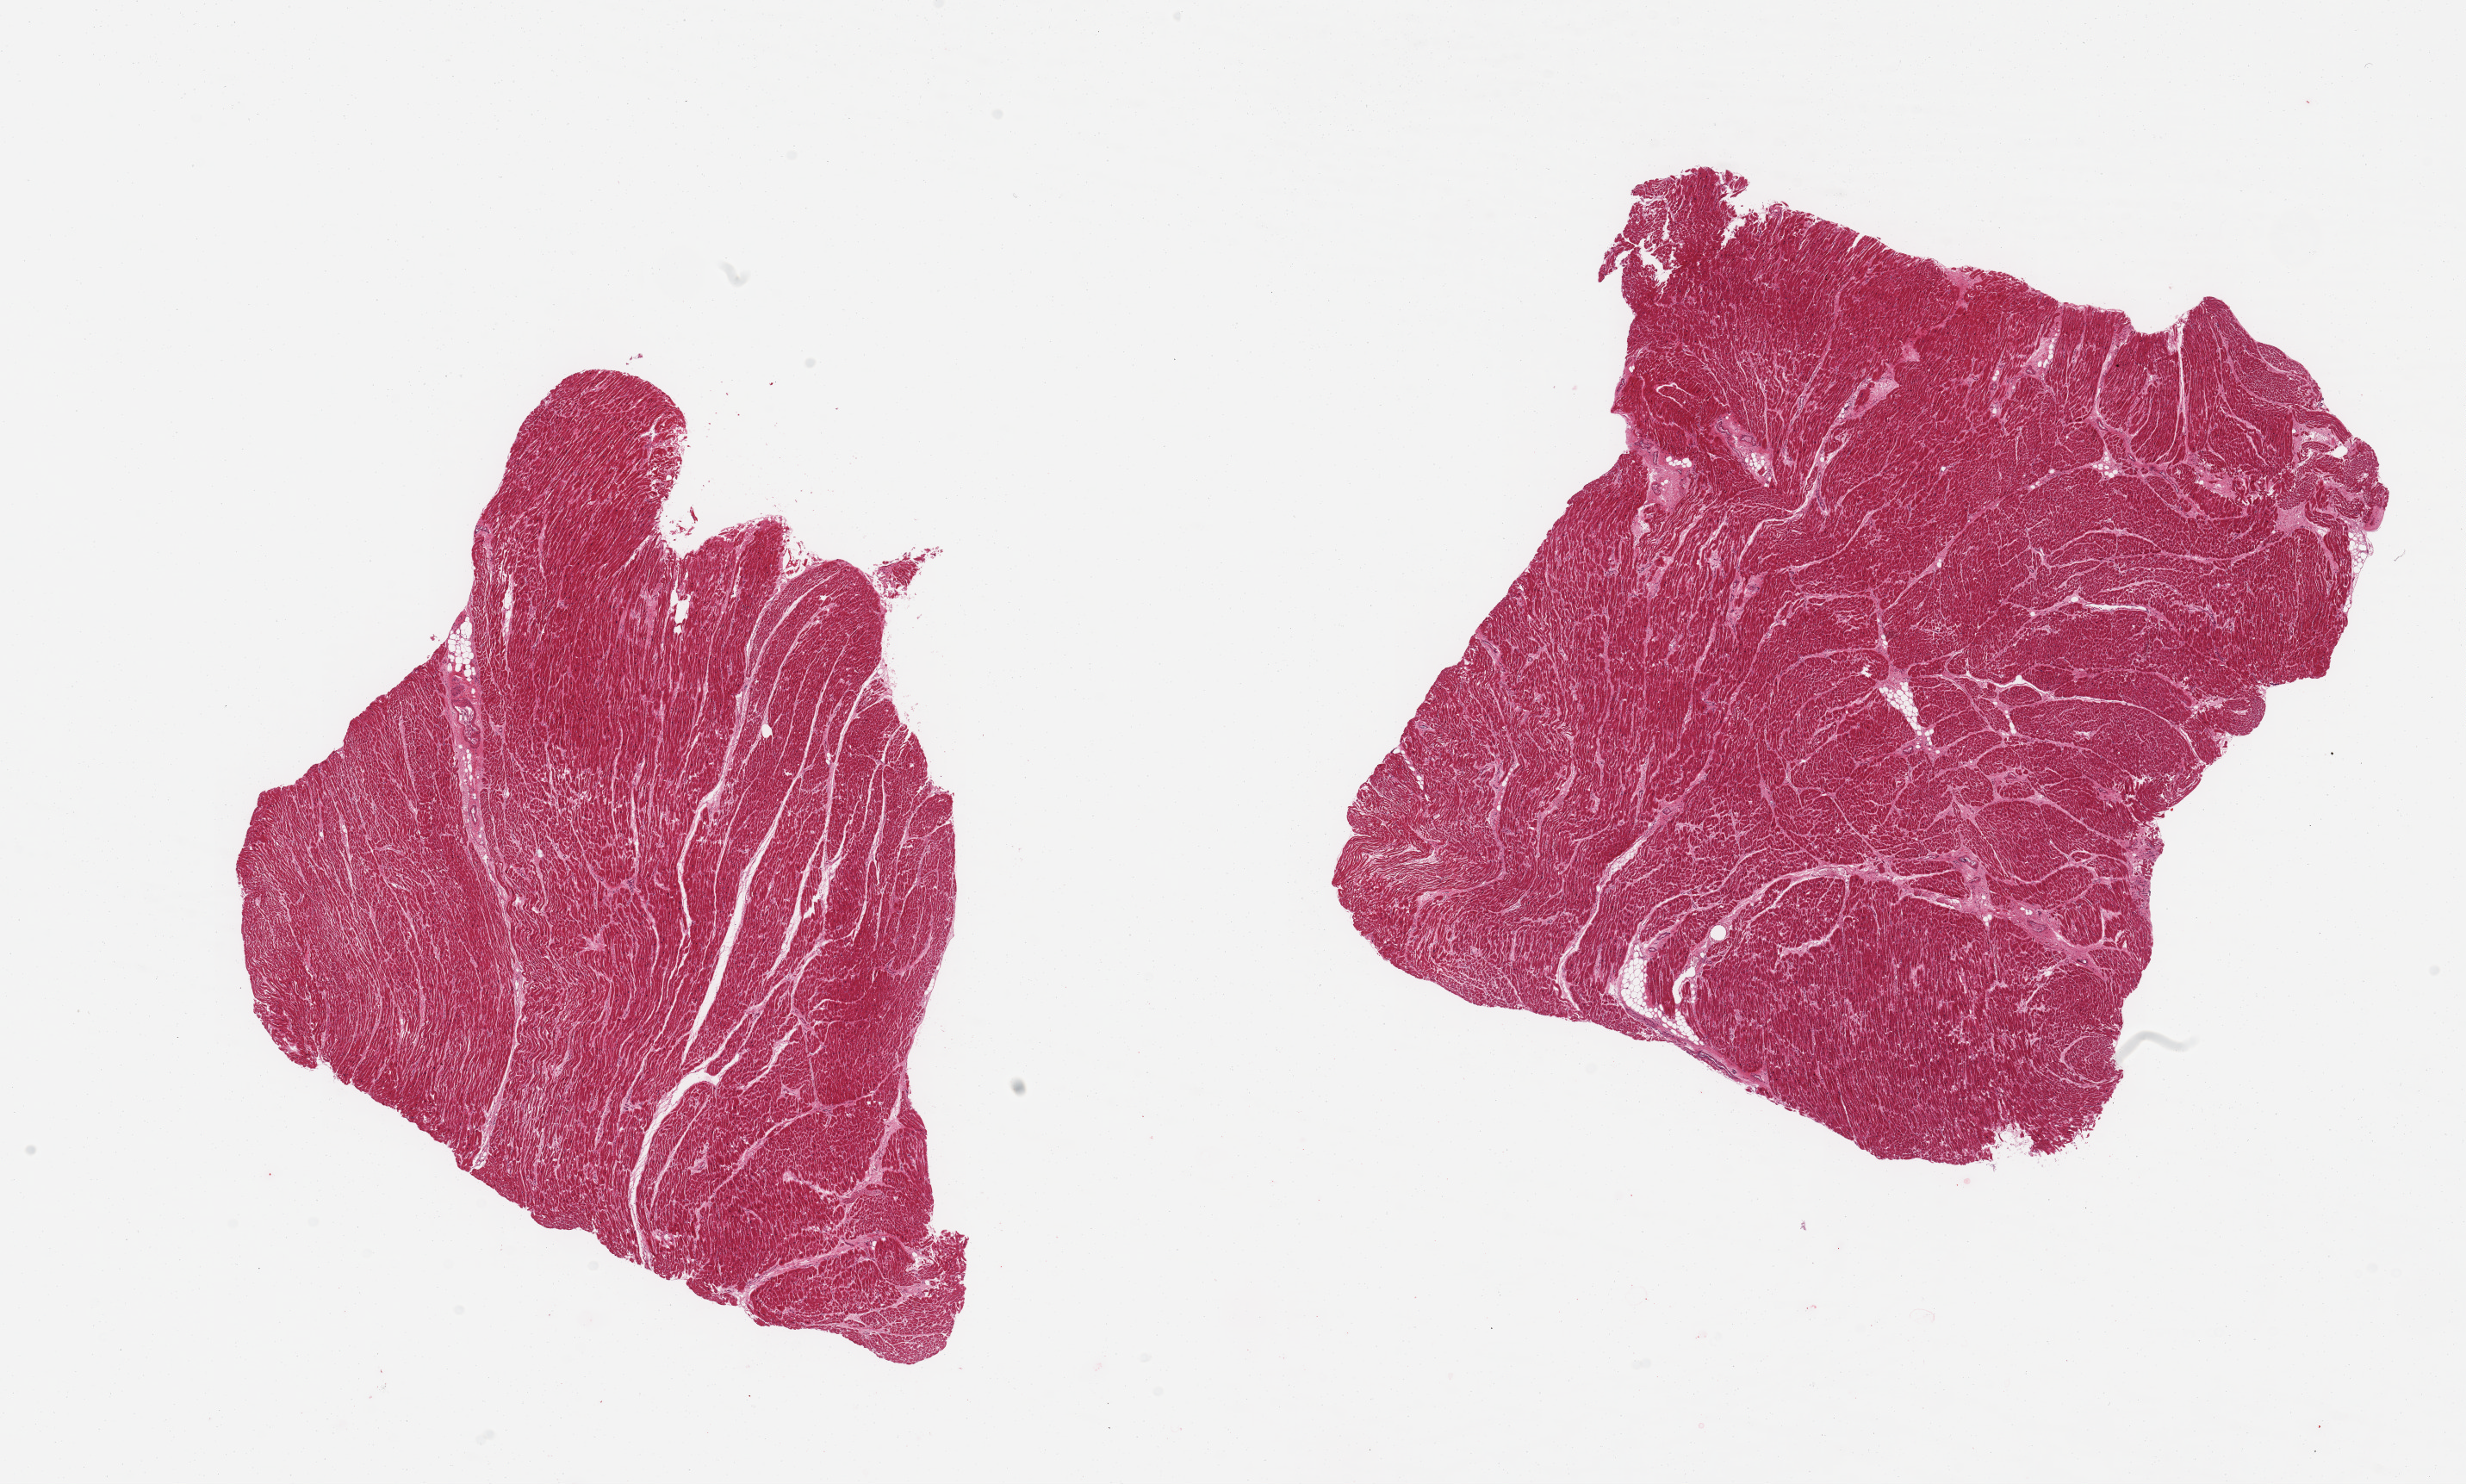
Whole-slide image, hematoxylin and eosin (H&E) stain, brightfield — shown as a low-resolution overview of the whole scanned area (about 22.6 x 13.6 mm); PAXgene-fixed, paraffin-embedded tissue; target tissue: heart; donor tissue sample.
Reviewer comment on this tissue sample: 2 pieces, mild-moderate interstitial fibrosis/chronic ischemic changes.